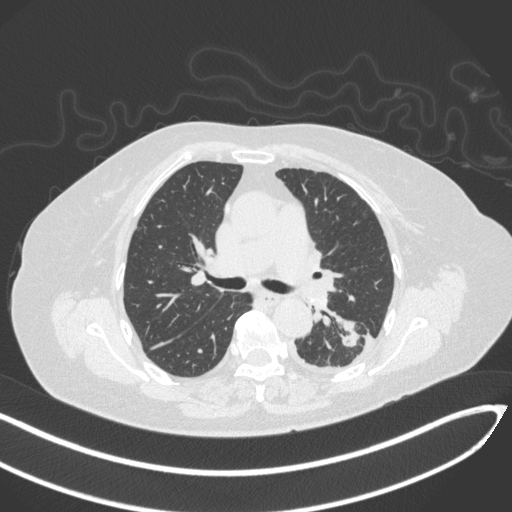
Chest CT, one axial slice. Reconstruction kernel B31f. 120 kVp. Lung window (W 1500 / L -600 HU). 512 × 512 image matrix. Patient: female, 76 years. Case-level facts recorded for this patient, not image findings: clinical TNM (as recorded): T1c N0 M0.
Structures marked on this image (bounding box drawn by a radiologist):
- lung tumour (recorded histology: adenocarcinoma): bounding box [x1, y1, x2, y2] px = [336, 323, 362, 351]